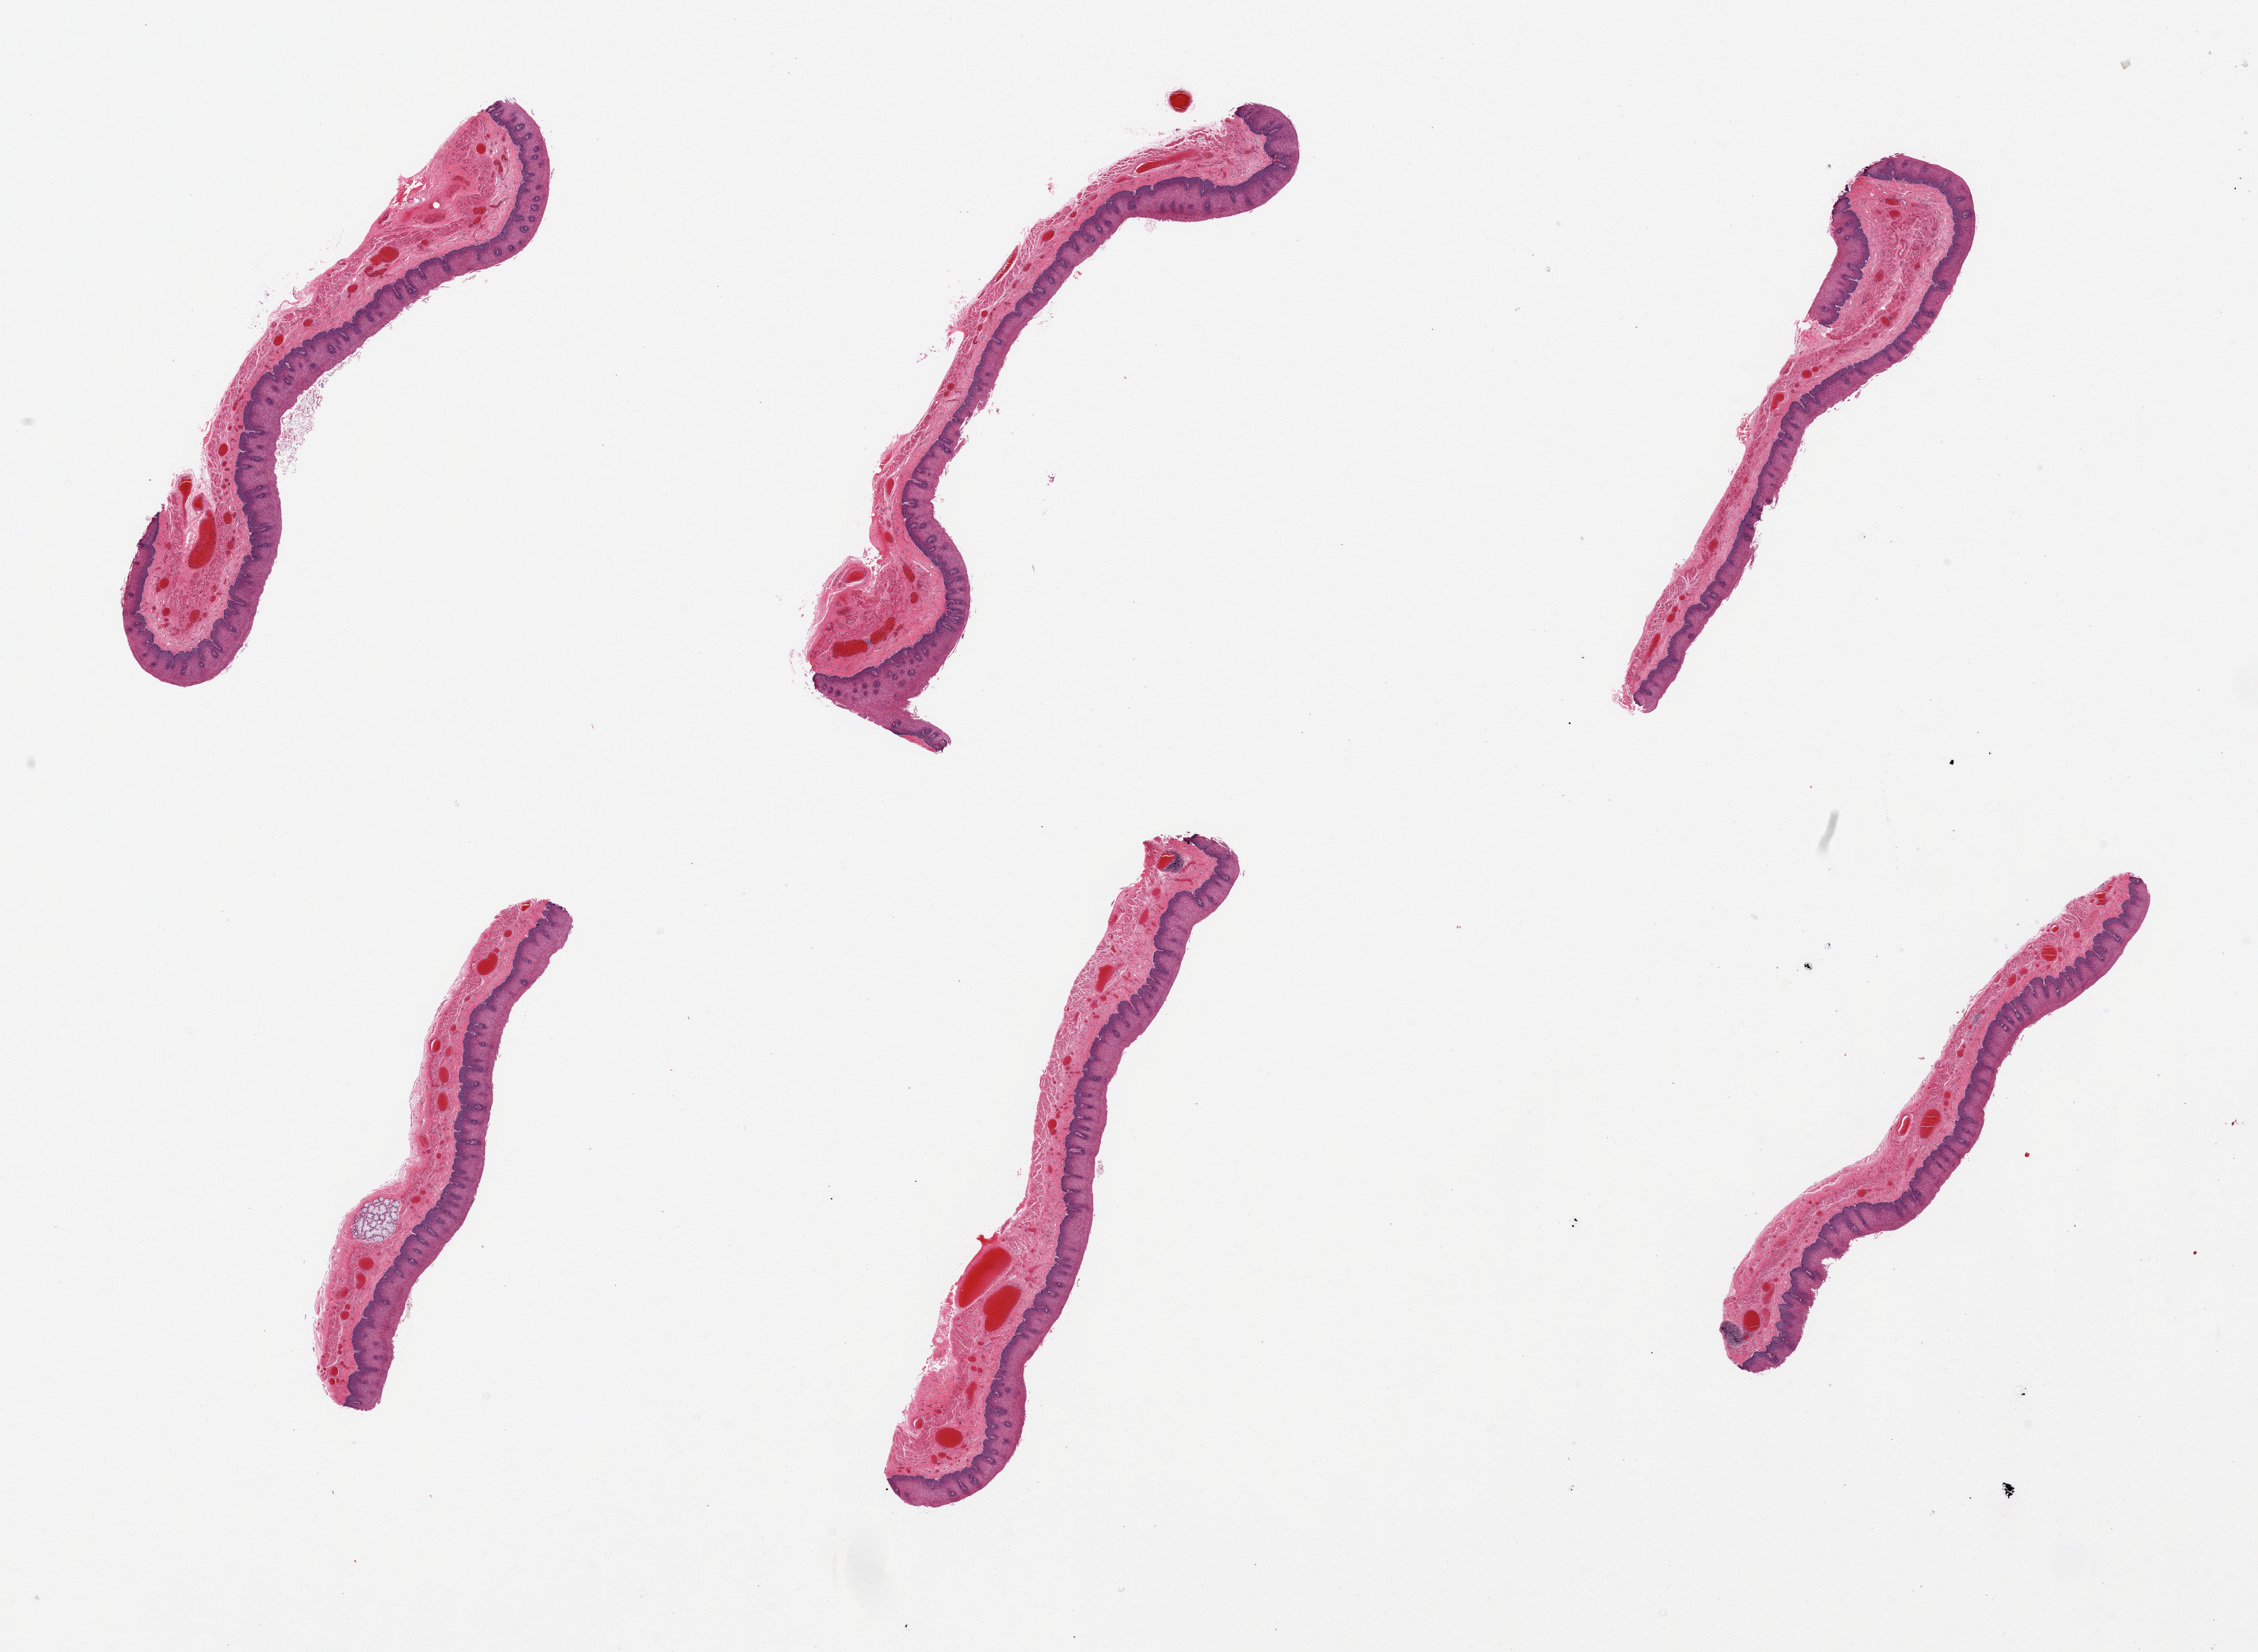
H&E whole-slide image — a low-resolution overview of the entire scanned area, about 26.6 x 19.4 mm (slide scanned at 20x). PAXgene-fixed paraffin-embedded (PFPE) section. Target tissue: esophageal mucous membrane. Tissue donor sample.
* pathologist's review note for this sample: 6 pieces; well dissected